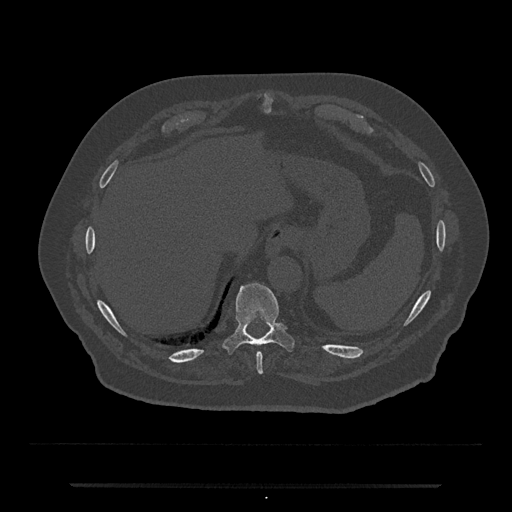
CT including the spine, one axial slice; slice 713 of 797 in the series (ordered by position); reconstruction kernel Br40s/3; 120 kVp; bone window (W 1800 / L 400 HU); 0.5 mm slice thickness; 512 × 512 image matrix. Male patient, age 80 years. From the clinical record (not read from this slice): primary cancer: prostate; vertebrae with lytic lesions (as recorded): L1, T11.
Outlined on this slice (semi-automatically segmented with operator editing):
- T10 vertebra: box from (x=224, y=283) to (x=294, y=353) px
- T9 vertebra: (x=256, y=353)–(x=263, y=374)